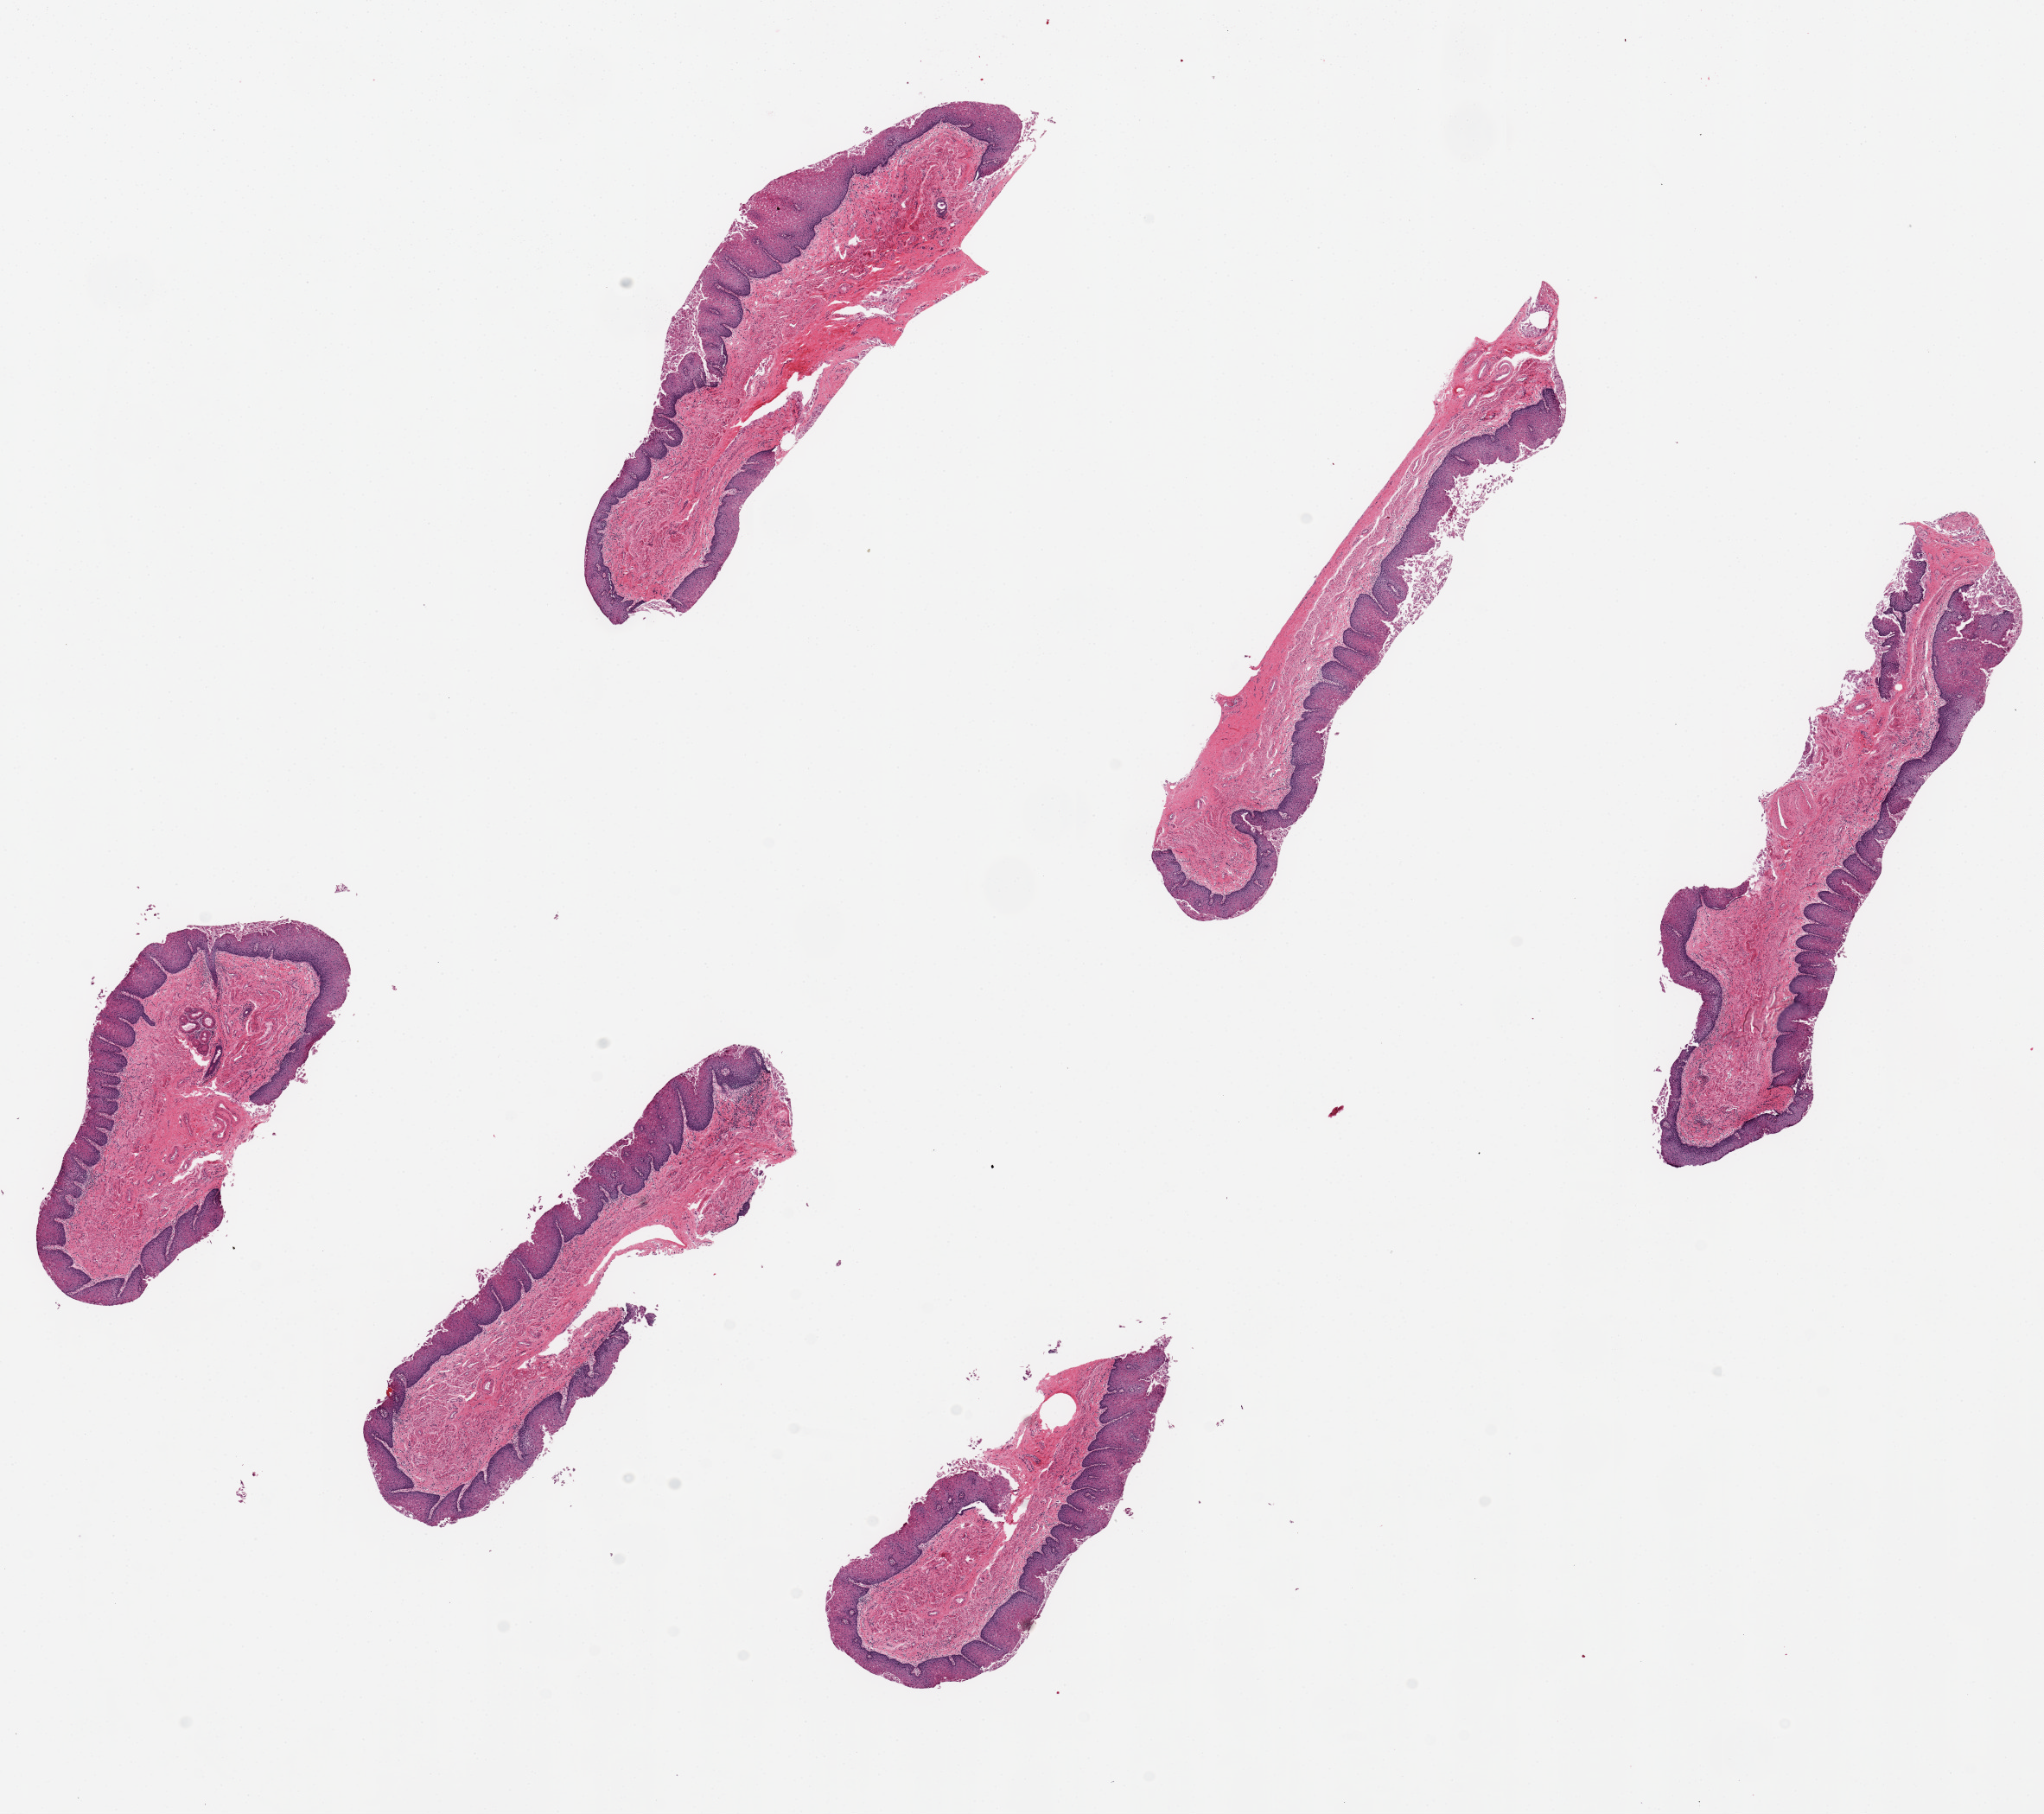
Whole-slide image, hematoxylin and eosin (H&E) stain, brightfield, a low-resolution overview of the entire scanned area, about 18.7 x 16.6 mm (slide scanned at 20x), PAXgene-fixed, paraffin-embedded tissue, target tissue: esophageal mucous membrane, tissue donor sample.
Pathologist's review note for this sample: 6 ~6x1mm pieces; squamous mucosa is 15-40% of thickness.